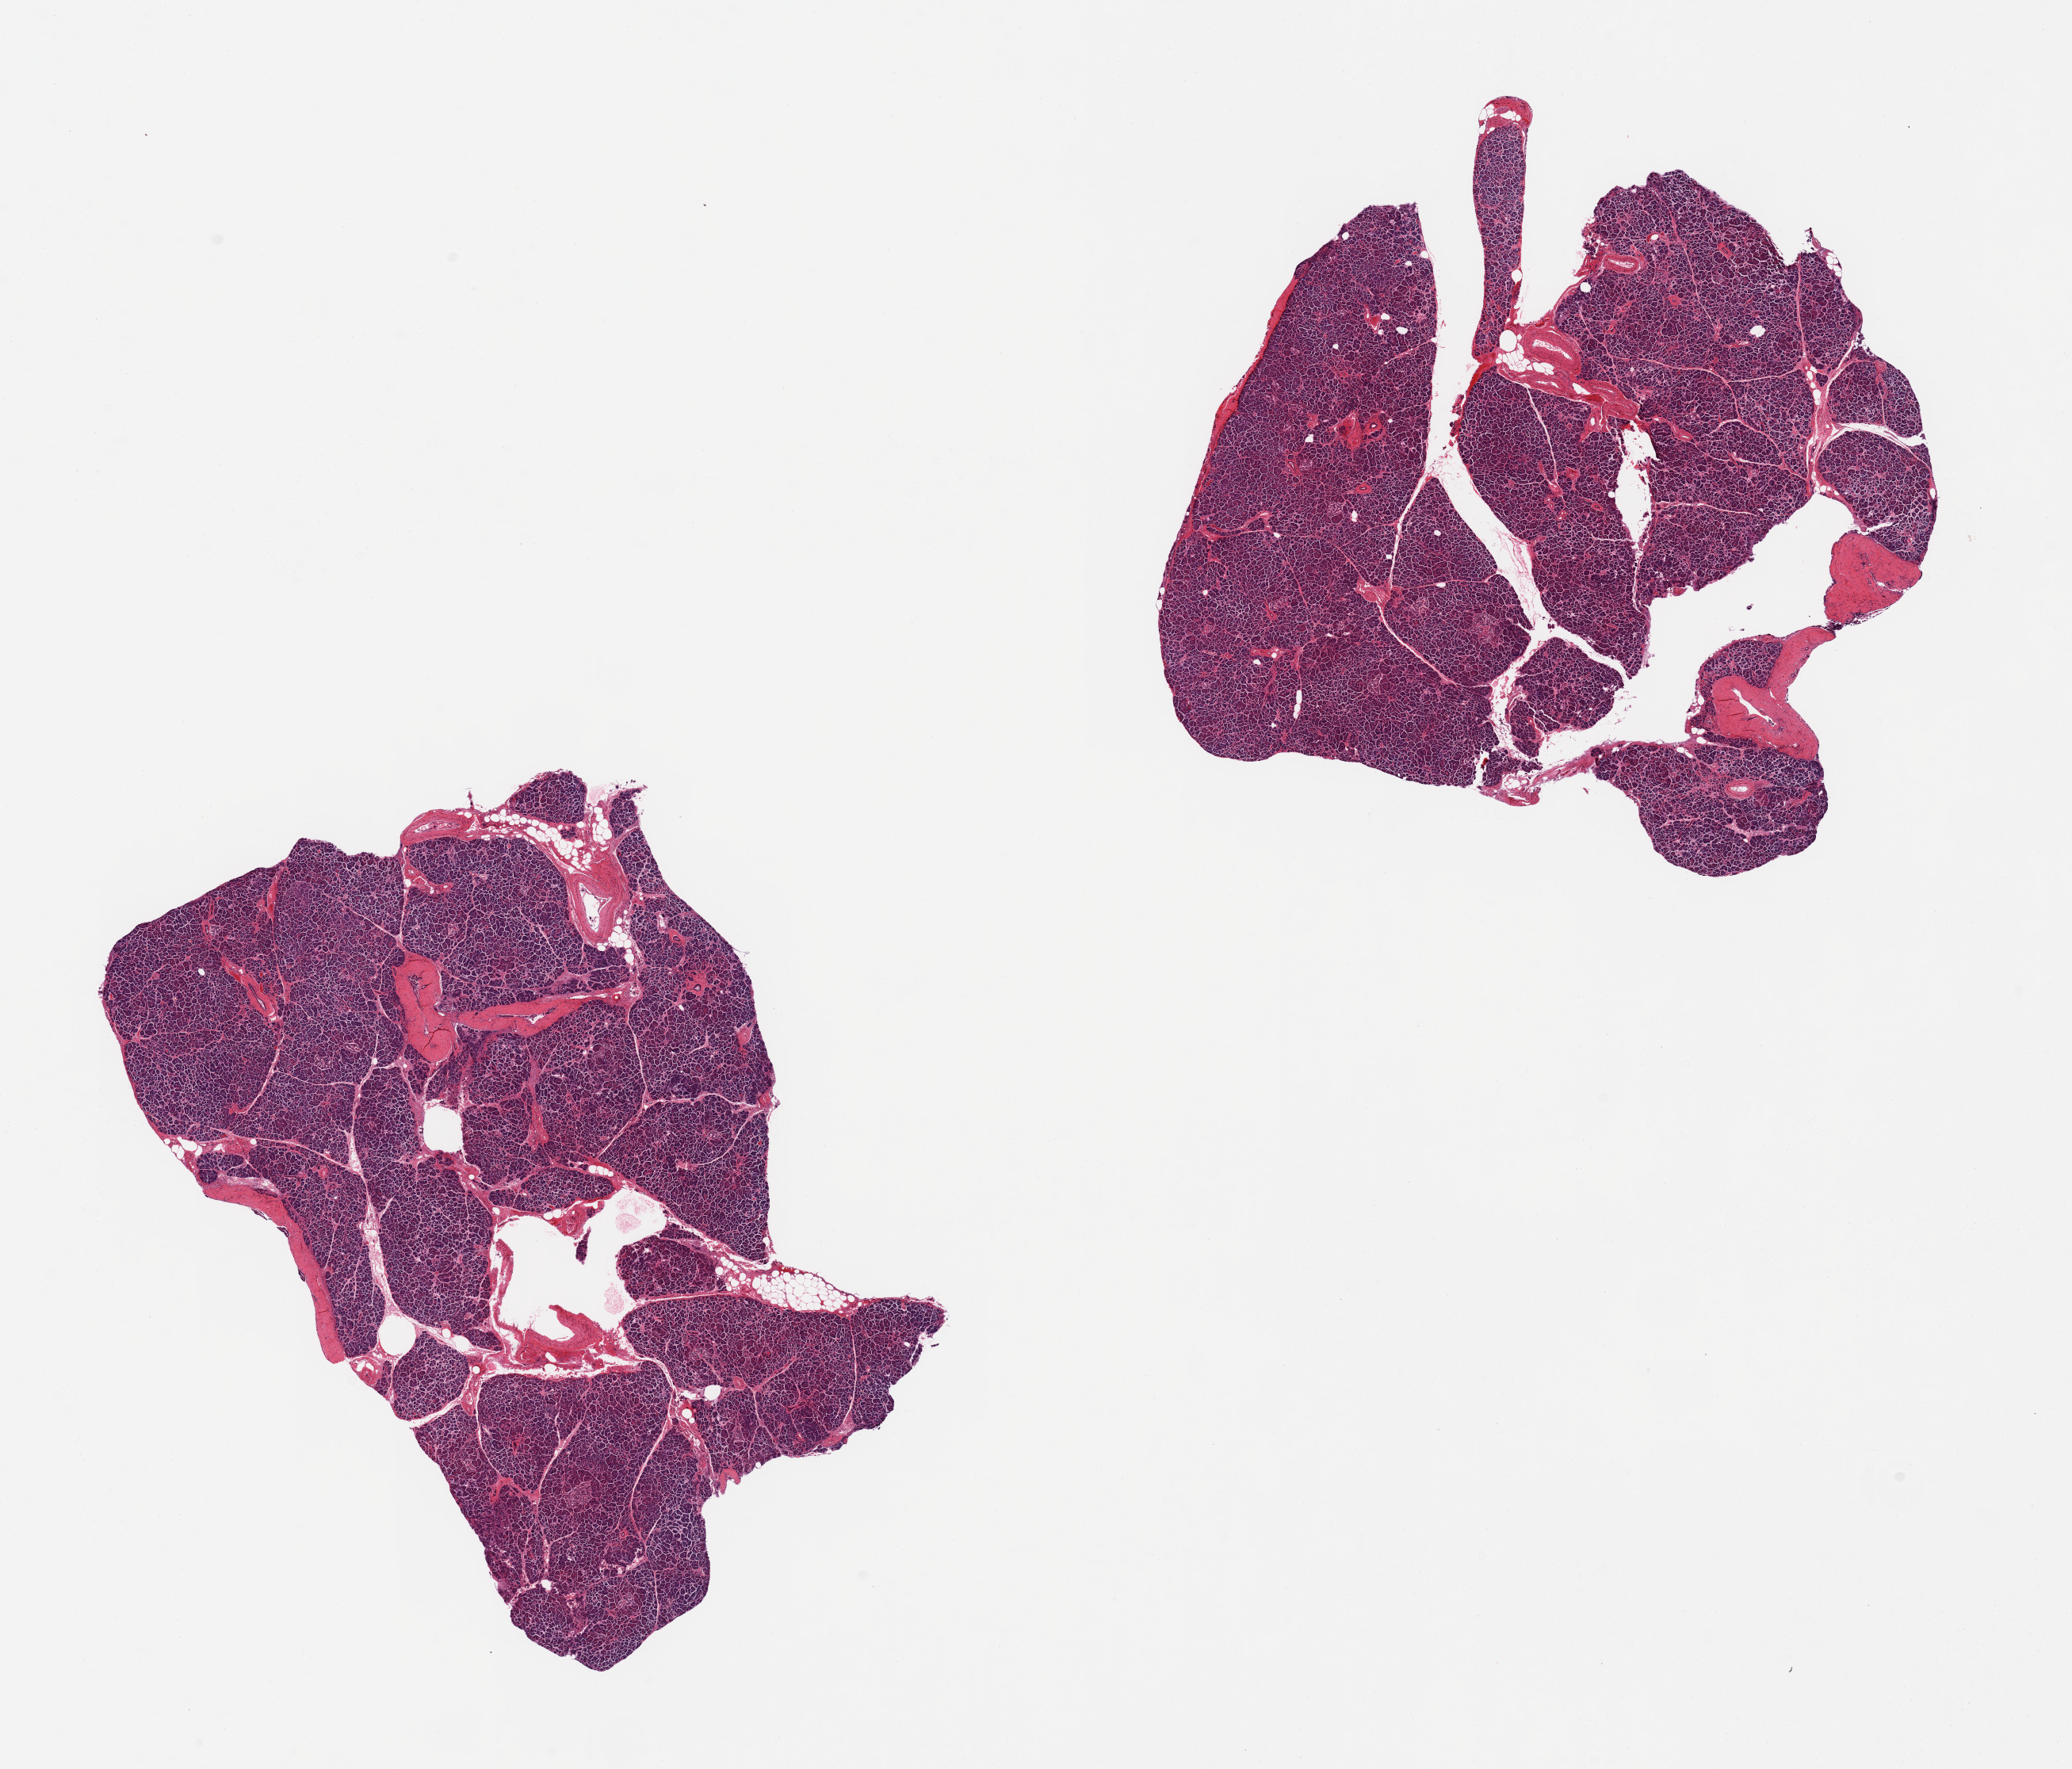
H&E whole-slide image, low-resolution overview of the scanned area, about 20.7 x 17.7 mm. PAXgene-fixed, paraffin-embedded tissue. Sampled site (target tissue): pancreas. Donor tissue sample. Donor sex: female.
Reviewer comment on this tissue sample: 2 pieces, minimal fat; Islets stil visible.